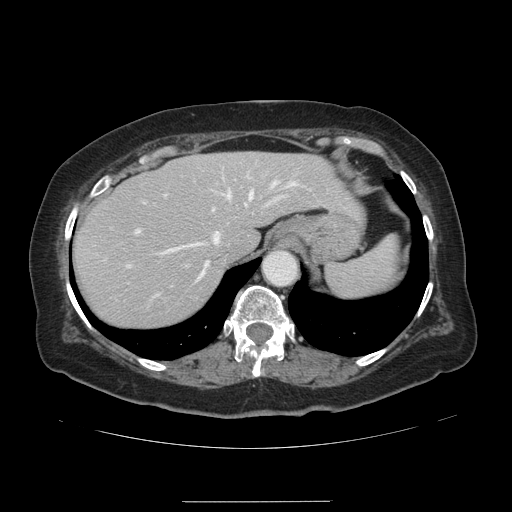
Contrast-enhanced abdominal CT, one axial slice. Slice 104 of 141 in the series (ordered by position). 120 kVp. Intravenous contrast given. Soft-tissue window (W 400 / L 40 HU). 2.5 mm slice thickness. 512 × 512 image matrix, field of view 393 × 393 mm. Female patient, age 74 years. From the clinical record (not read from this slice): diagnosis: colorectal cancer liver metastases, imaged before liver resection.
Structures marked on this image (manually delineated by an expert):
- hepatic veins: bounding box [x1, y1, x2, y2] px = [154, 181, 294, 282]
- liver: [72, 152, 359, 329]
- planned liver remnant (the part of the liver to remain after resection): [72, 152, 359, 329]
- portal vein (with intrahepatic branches): [127, 173, 280, 296]